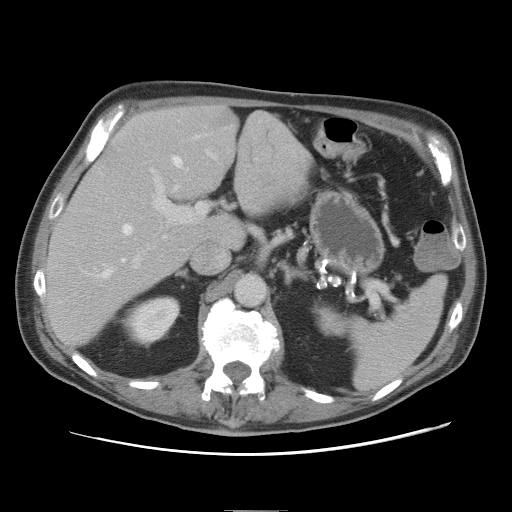
Contrast-enhanced abdominal CT, one axial slice; slice 47 of 89 in the series (ordered by position); intravenous contrast given; soft-tissue window (W 400 / L 40 HU); 512 × 512 image matrix. Male patient, age 69 years. From the clinical record (not read from this slice): diagnosis: colorectal cancer liver metastases, imaged before liver resection; multiple liver metastases: no; largest metastasis: 8.5 cm; chemotherapy before resection: no.
Outlined on this slice (manually delineated by an expert):
- hepatic veins: bounding box [x1, y1, x2, y2] px = [102, 136, 200, 277]
- liver: [46, 107, 308, 343]
- planned liver remnant (the part of the liver to remain after resection): [46, 107, 243, 343]
- portal vein (with intrahepatic branches): [134, 150, 216, 267]